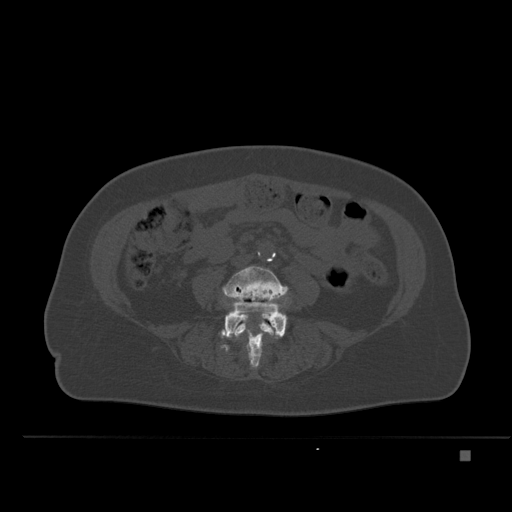
CT including the spine, one axial slice; slice 170 of 477 in the series (ordered by position); bone window (W 1800 / L 400 HU); 512 × 512 image matrix, field of view 422 × 422 mm. Patient: female, 74 years. Case-level facts recorded for this patient, not image findings: primary cancer: colon.
Structures marked on this image (semi-automatic segmentation, software-assisted and operator-edited):
- L4 vertebra: bounding box <223,266,288,353> (left, top, right, bottom; pixels)
- L5 vertebra: <221,298,288,368>